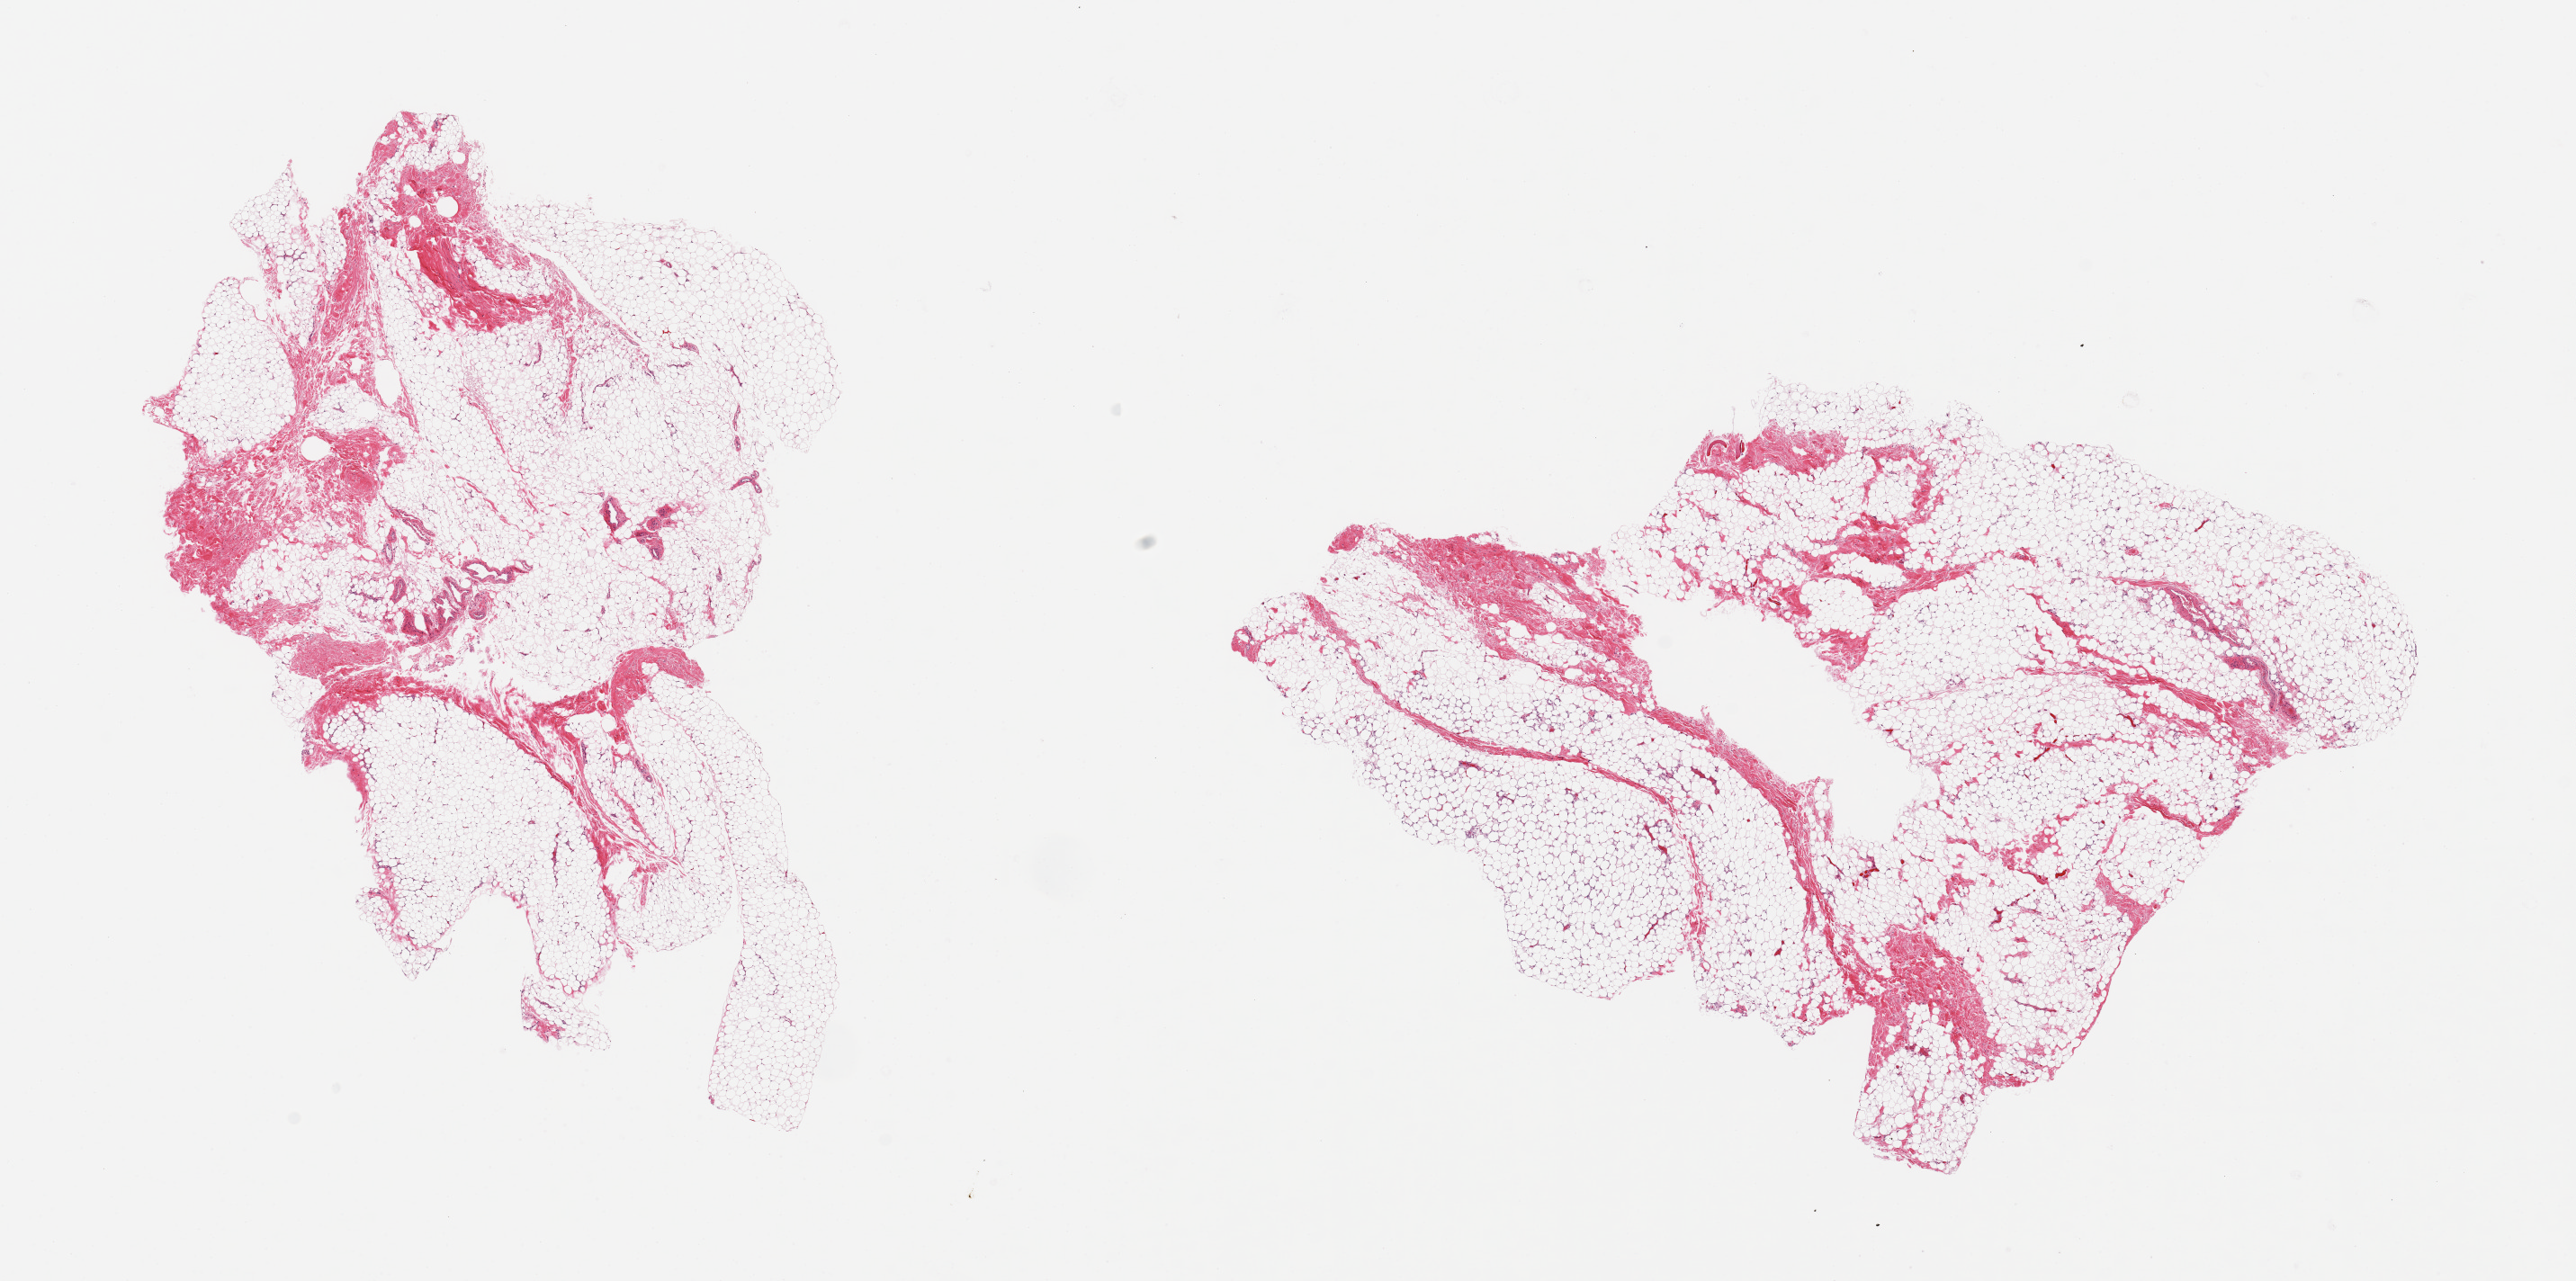
Haematoxylin and eosin whole-slide image — low-resolution overview of the scanned area, about 22.6 x 11.3 mm; PAXgene-fixed paraffin-embedded (PFPE) section; target tissue: breast; donor tissue sample. Donor: male.
Review note (as recorded): 2 pieces, fibroadipose tissue, no ductal elements.